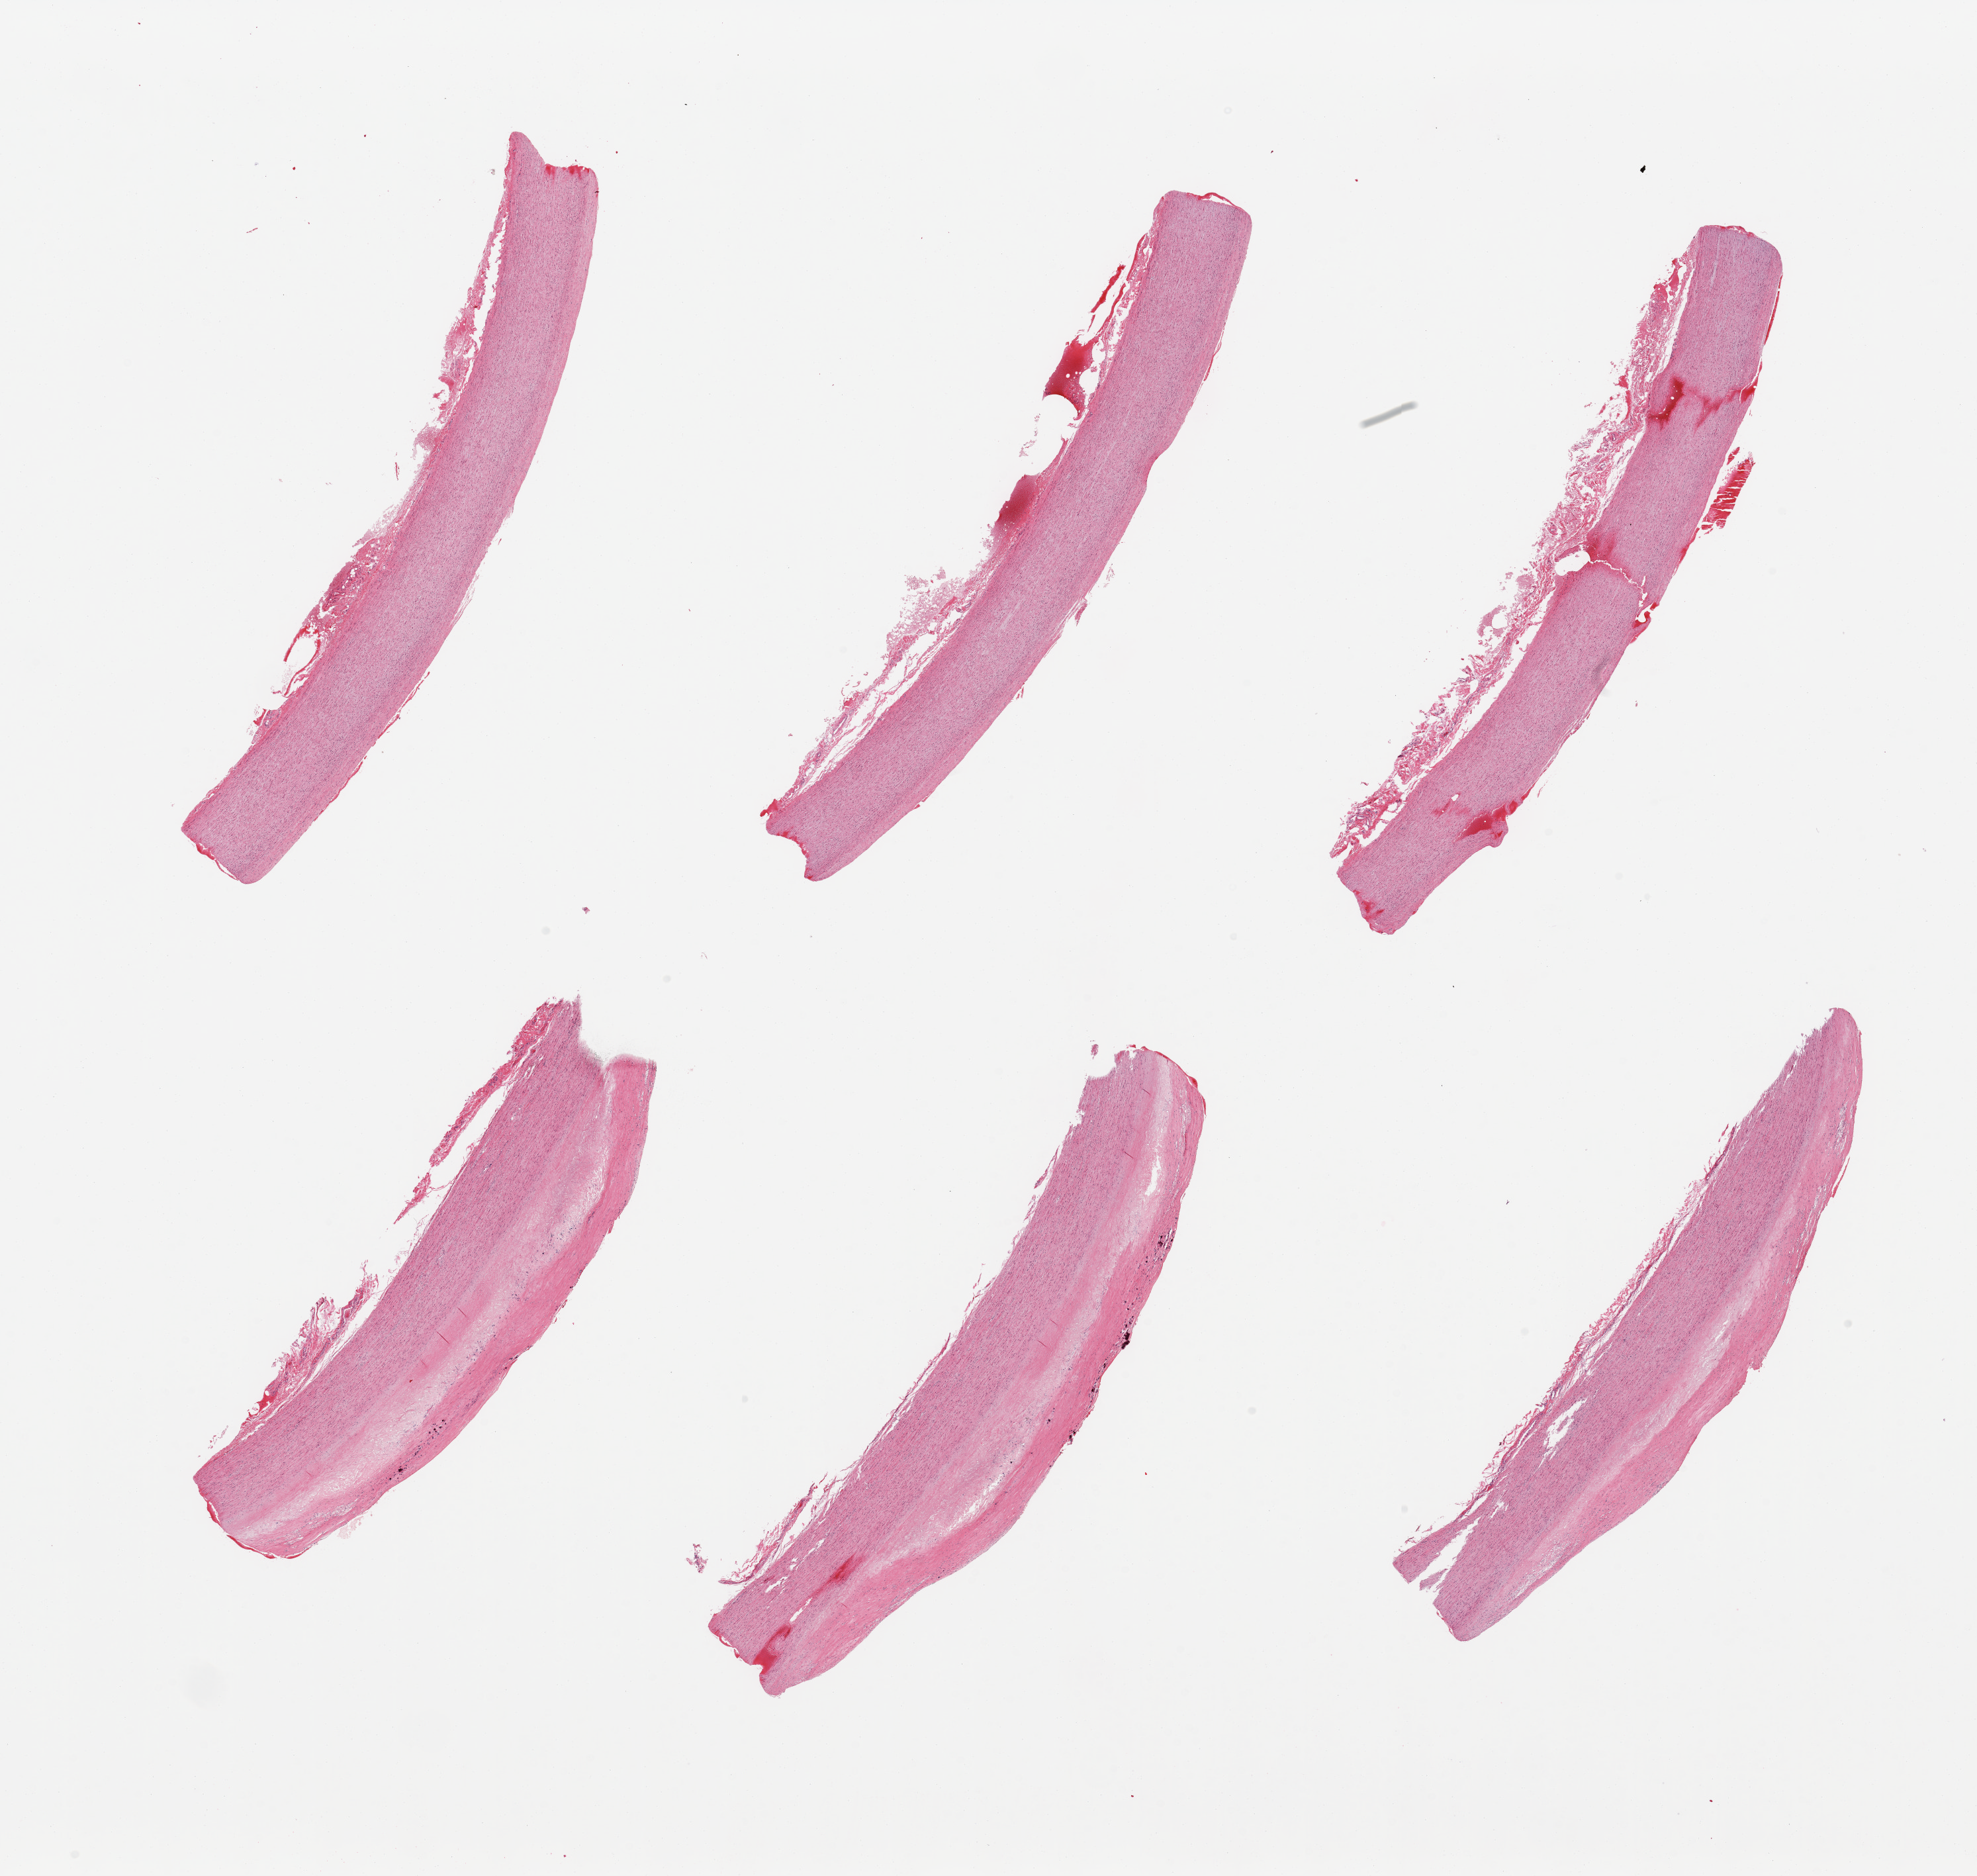
Digitized H&E-stained section, brightfield — a low-resolution overview of the entire scanned area, about 23.6 x 22.4 mm; PAXgene-fixed, paraffin-embedded tissue; target tissue: aorta; tissue donor sample. Donor: female.
Pathologist's review note for this sample: 6 pieces; atherosclerosis, some calcification.